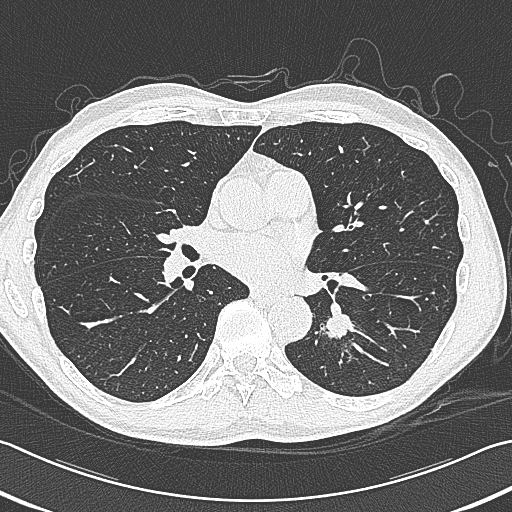
Chest CT (low-dose screening protocol), one axial image. First (baseline) screen. Lung window (W 1500 / L -600 HU). Slice 178 of 354 in the series. 512 × 512 image matrix. Male participant, aged 59 years at enrolment.
Lesion marked by an expert reader, bounding box (x1, y1, x2, y2) in pixels: (312, 295, 375, 353). Screening reader's record for this exam (one nodule recorded; not confirmed to be the boxed lesion): non-calcified nodule or mass ≥4 mm, left lower lobe, 15 × 15 mm, smooth margins, soft tissue attenuation. Official screen result: positive, change unspecified: nodule(s) >= 4 mm or enlarging nodule(s), mass(es), or other non-specific abnormalities suspicious for lung cancer. Later outcome: lung cancer diagnosed 17 days after this screen — squamous cell carcinoma, large cell, nonkeratinizing, NOS, left lower lobe, poorly differentiated (G3), stage IB (AJCC 6th edition), 31 mm at pathology.